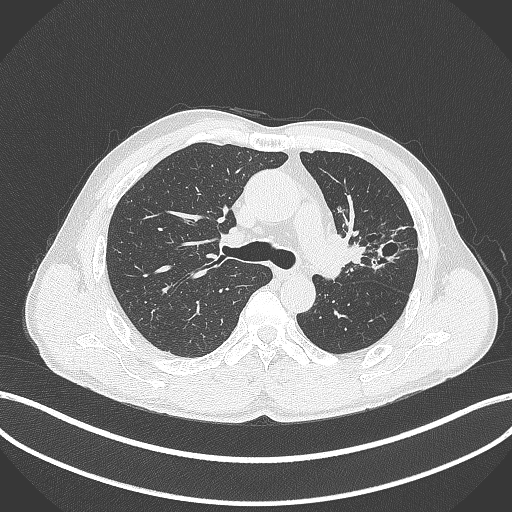
Chest CT, one axial slice. Slice 272 of 429 in the series (ordered by position). Reconstruction kernel B70f. Lung window (W 1500 / L -600 HU). 1 mm slice thickness. 512 × 512 image matrix, field of view 400 × 400 mm. Patient: male, 57 years. From the clinical record (not read from this slice): clinical TNM (as recorded): T2b N0 M0.
Outlined on this slice (bounding box drawn by a radiologist):
- lung tumour (recorded histology: squamous cell carcinoma): box from (x=329, y=228) to (x=369, y=267) px